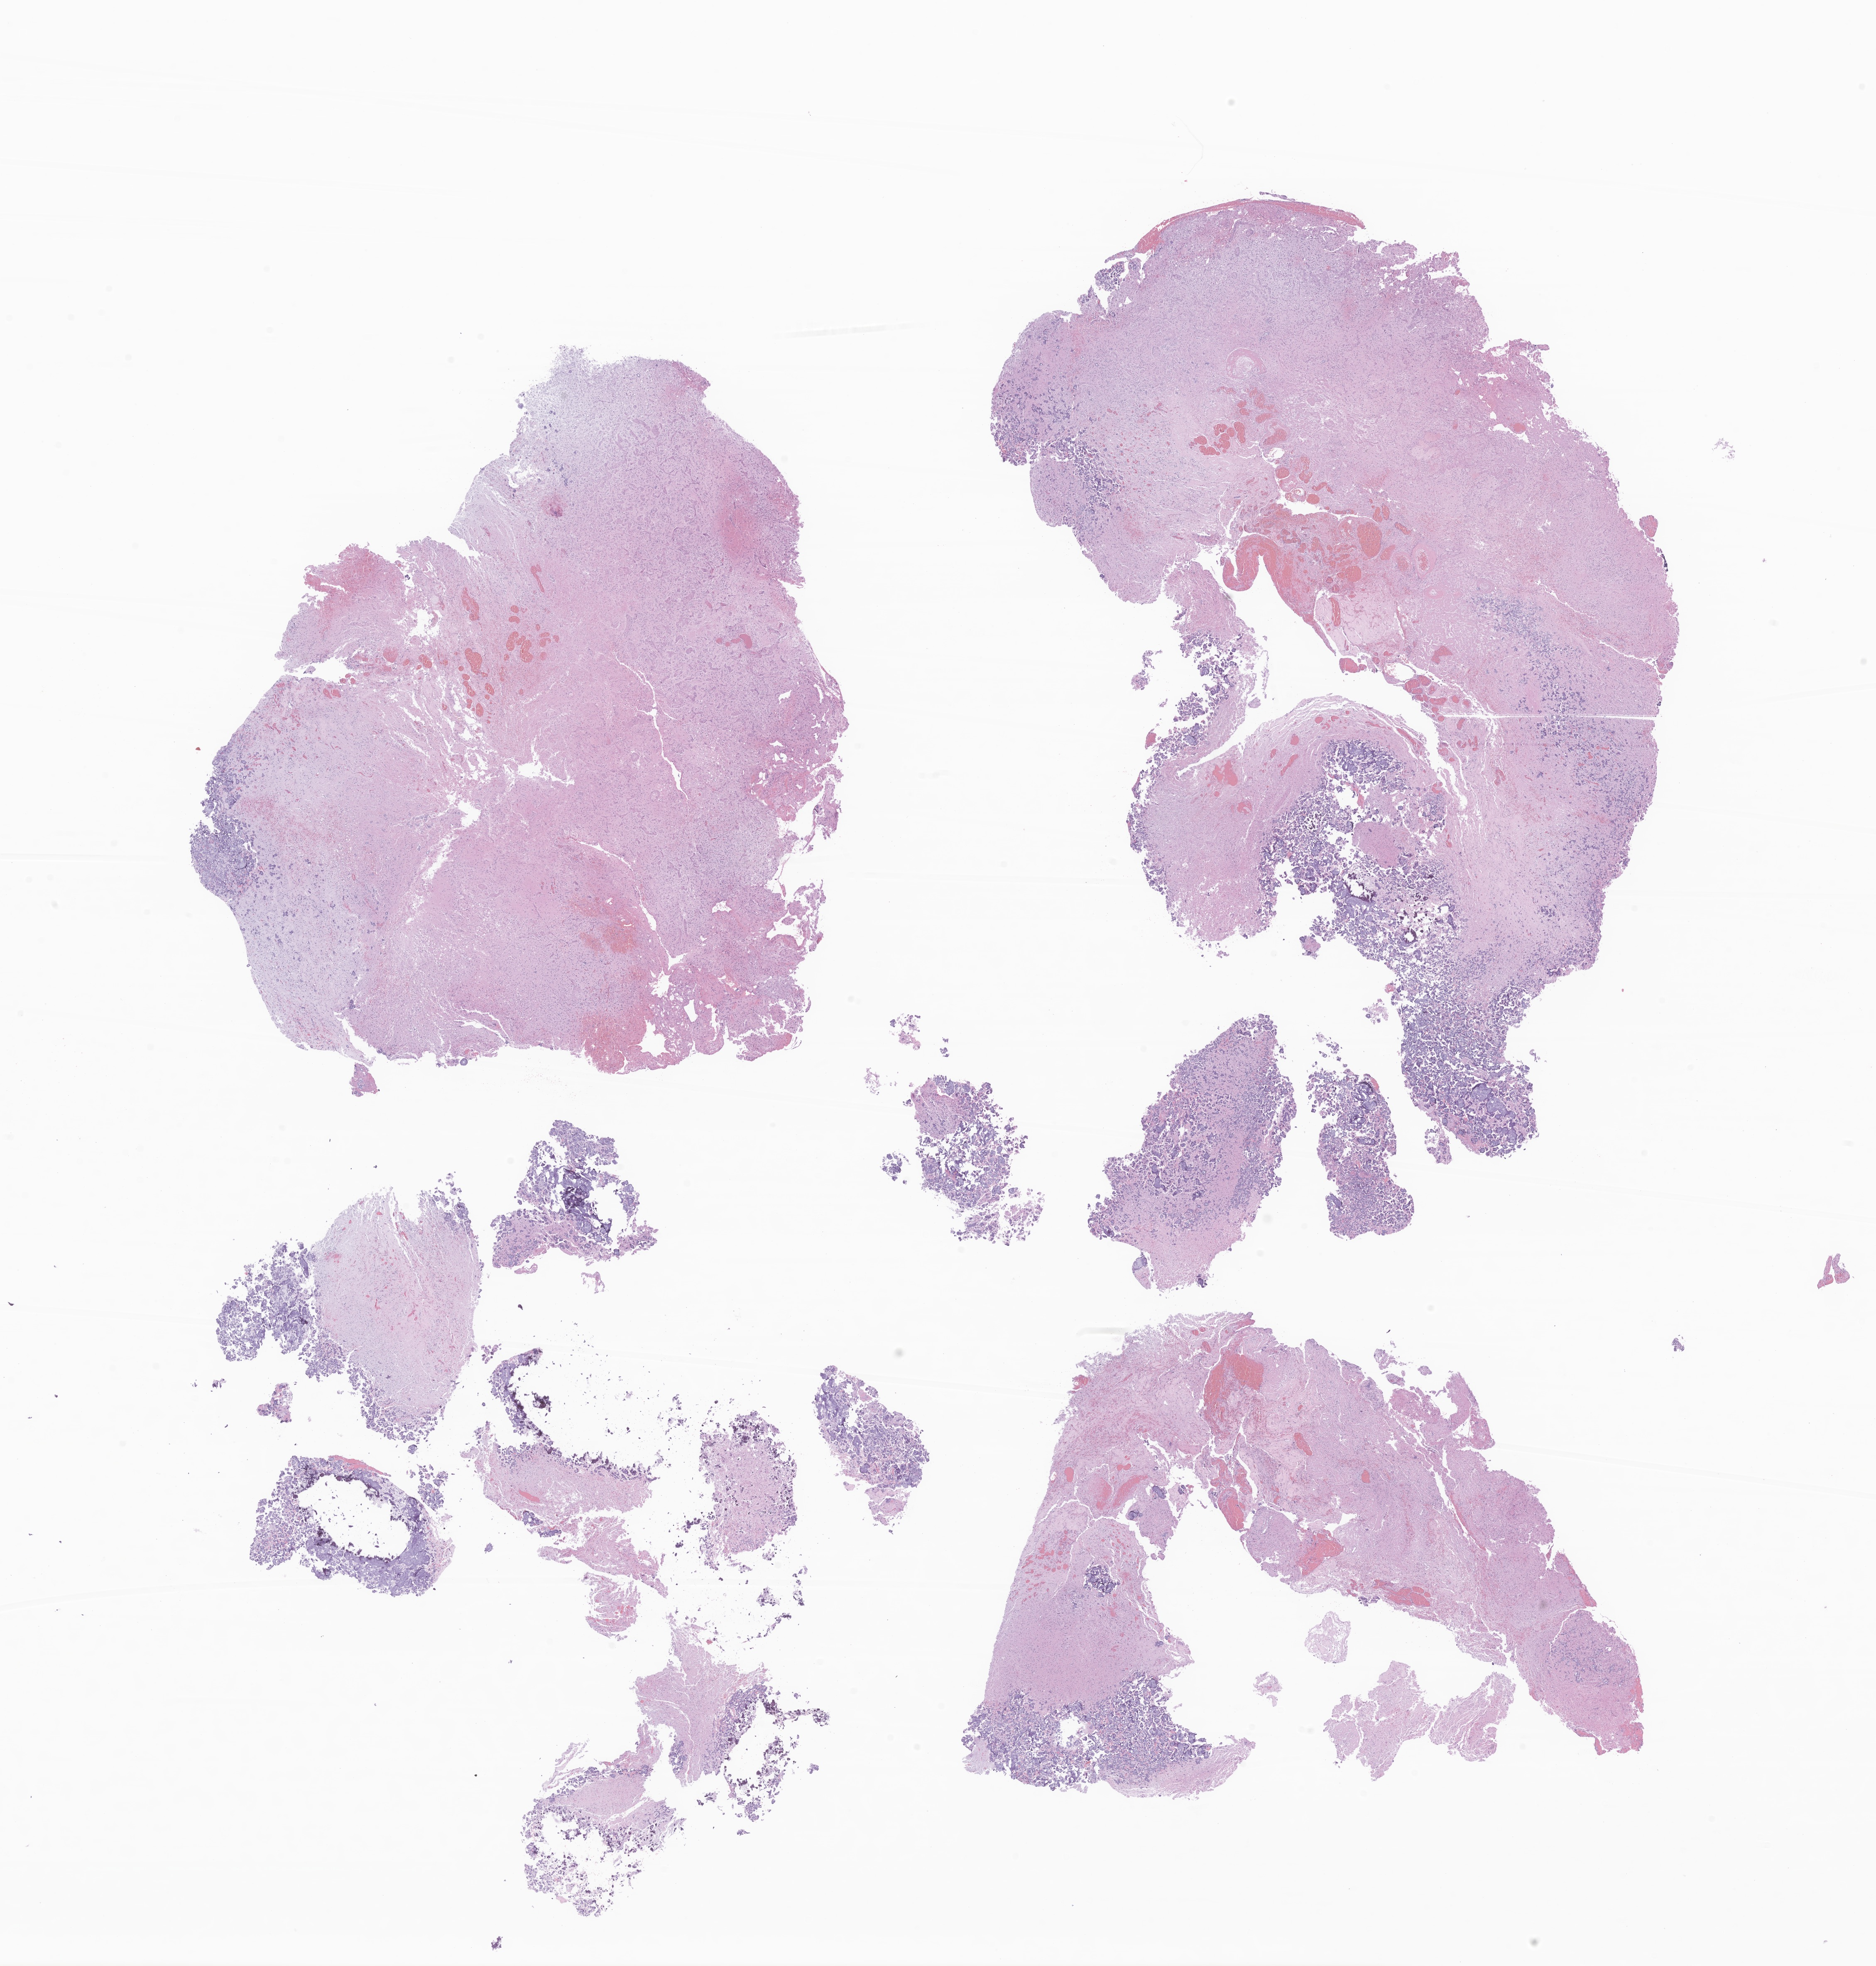
Digitized haematoxylin and eosin-stained section of tumor tissue from the brain — a low-resolution overview of the entire scanned area, about 19.0 x 20.0 mm, formalin-fixed, paraffin-embedded (FFPE) tissue. Patient male; age 132 months (11 years).
Diagnosis (ICD-O-3 morphology term): Tumor cells, uncertain whether benign or malignant.